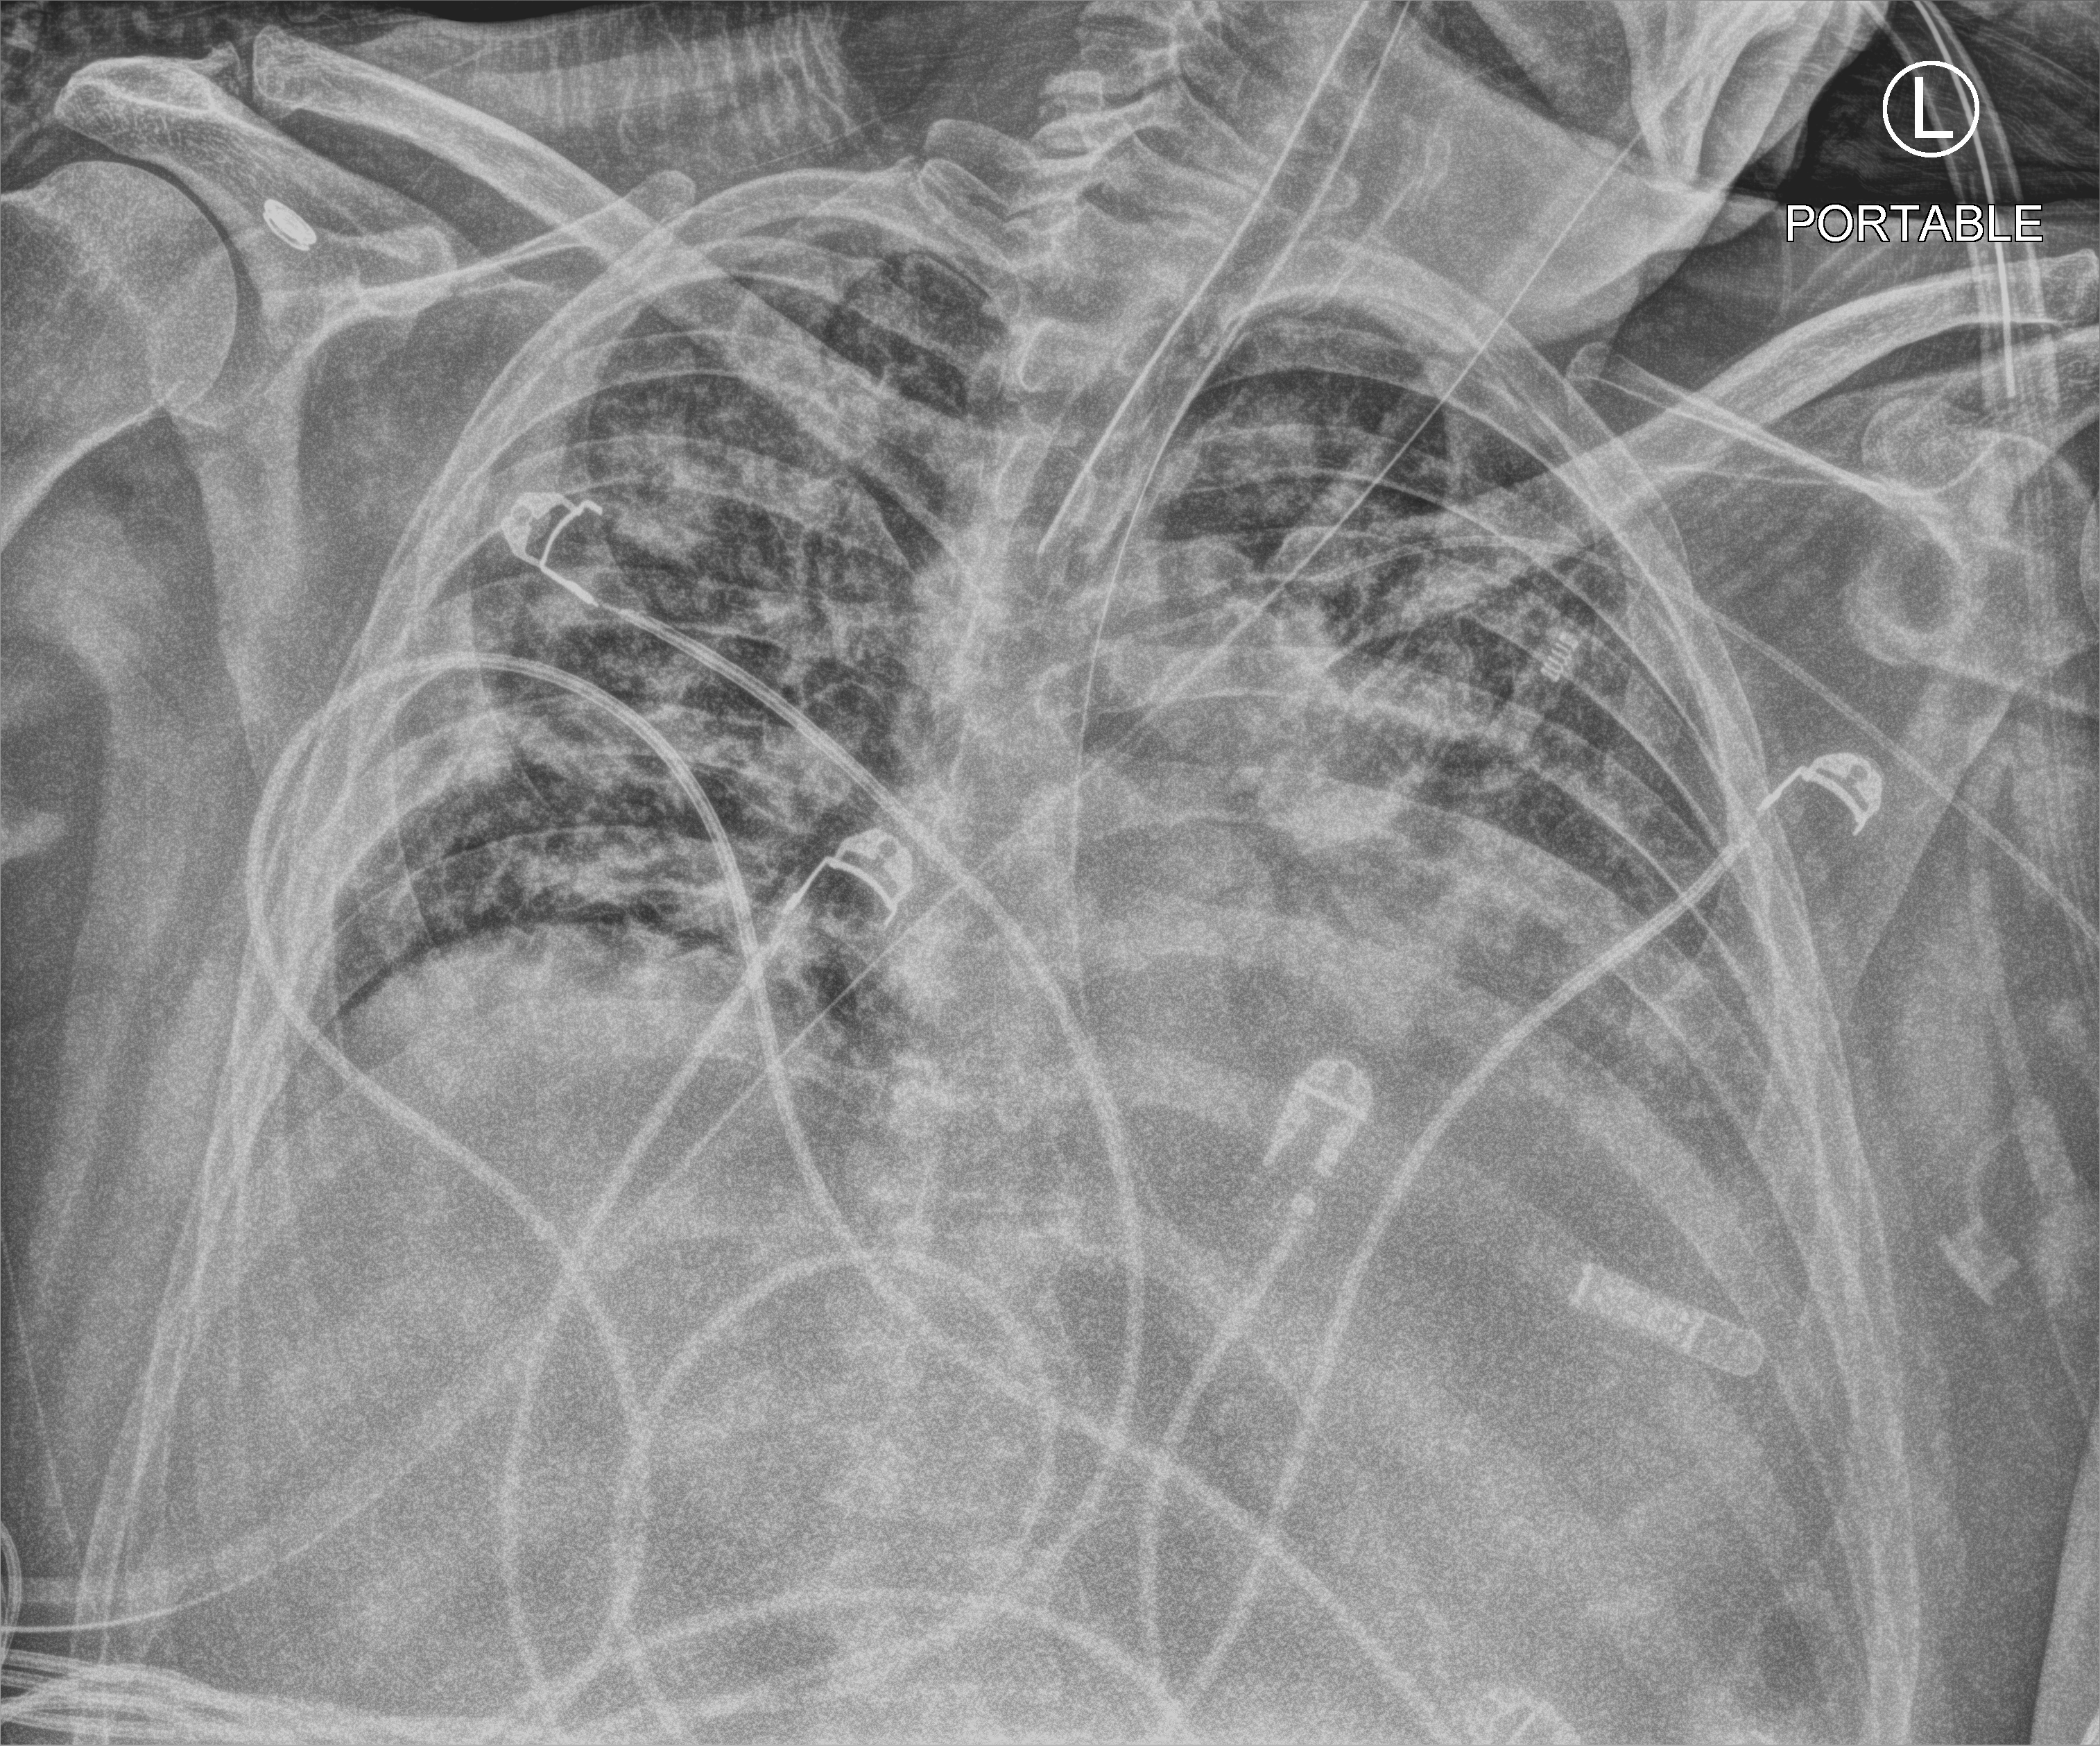
Chest X-ray (portable), anteroposterior (AP) projection. Male patient hospitalised with COVID-19, age 18–59 years.
Hospital-stay facts (about this admission, not read from this image; timing relative to this image not recorded):
- admitted to intensive care during this hospital stay: yes